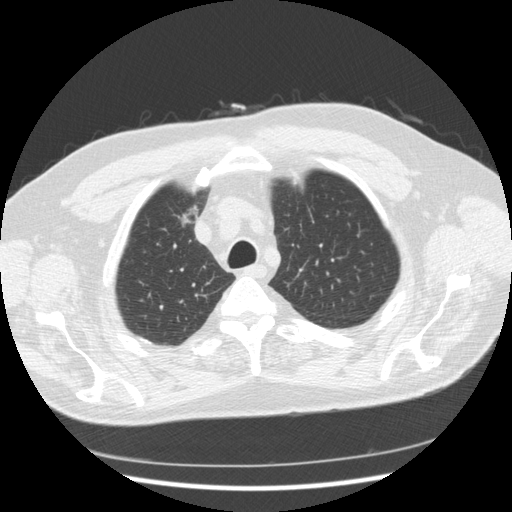
Axial slice from a low-dose chest CT screening exam. Second screening round (one year after baseline). Lung window (W 1500 / L -600 HU). Standard (soft-tissue) reconstruction kernel (STANDARD). 120 kVp. Slice 44 of 267 in the series. 512 × 512 image matrix, field of view 360 × 360 mm. Male participant, aged 66 years at enrolment. Former smoker at enrolment.
Lesion marked by an expert reader, bounding box <158,199,210,240> (left, top, right, bottom; pixels). No non-calcified nodule or mass ≥4 mm was recorded by the screening reader at this exam. Official screen result: positive, other. Participant outcome: lung cancer diagnosed 603 days after this screen — bronchiolo-alveolar adenocarcinoma, NOS, right upper lobe, moderately differentiated (G2), stage IA (AJCC 6th edition), 12 mm at pathology.